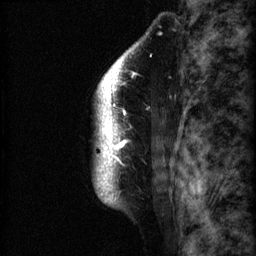
Breast MRI (dynamic contrast-enhanced), one sagittal slice; position 54 of 60 along the scan axis; 3 images stored at this slice position (order not interpretable as contrast timing); 1.5 T; TE 4.2 ms, TR 22.7 ms; 256 × 256 image matrix, field of view 180 × 180 mm. Female patient, age 48 years. Case-level facts recorded for this patient, not image findings: setting: breast cancer imaged before/during neoadjuvant chemotherapy; receptor status: triple-negative.
Outlined on this slice (semi-automatically segmented with operator editing):
- analysis volume of interest (the breast-tissue region the enhancement analysis was run in; not a lesion): bounding box [x1, y1, x2, y2] px = [92, 30, 173, 207]
- tumour enhancement mask (voxels above the 90 % enhancement threshold inside the analysis volume of interest): [94, 43, 143, 203]